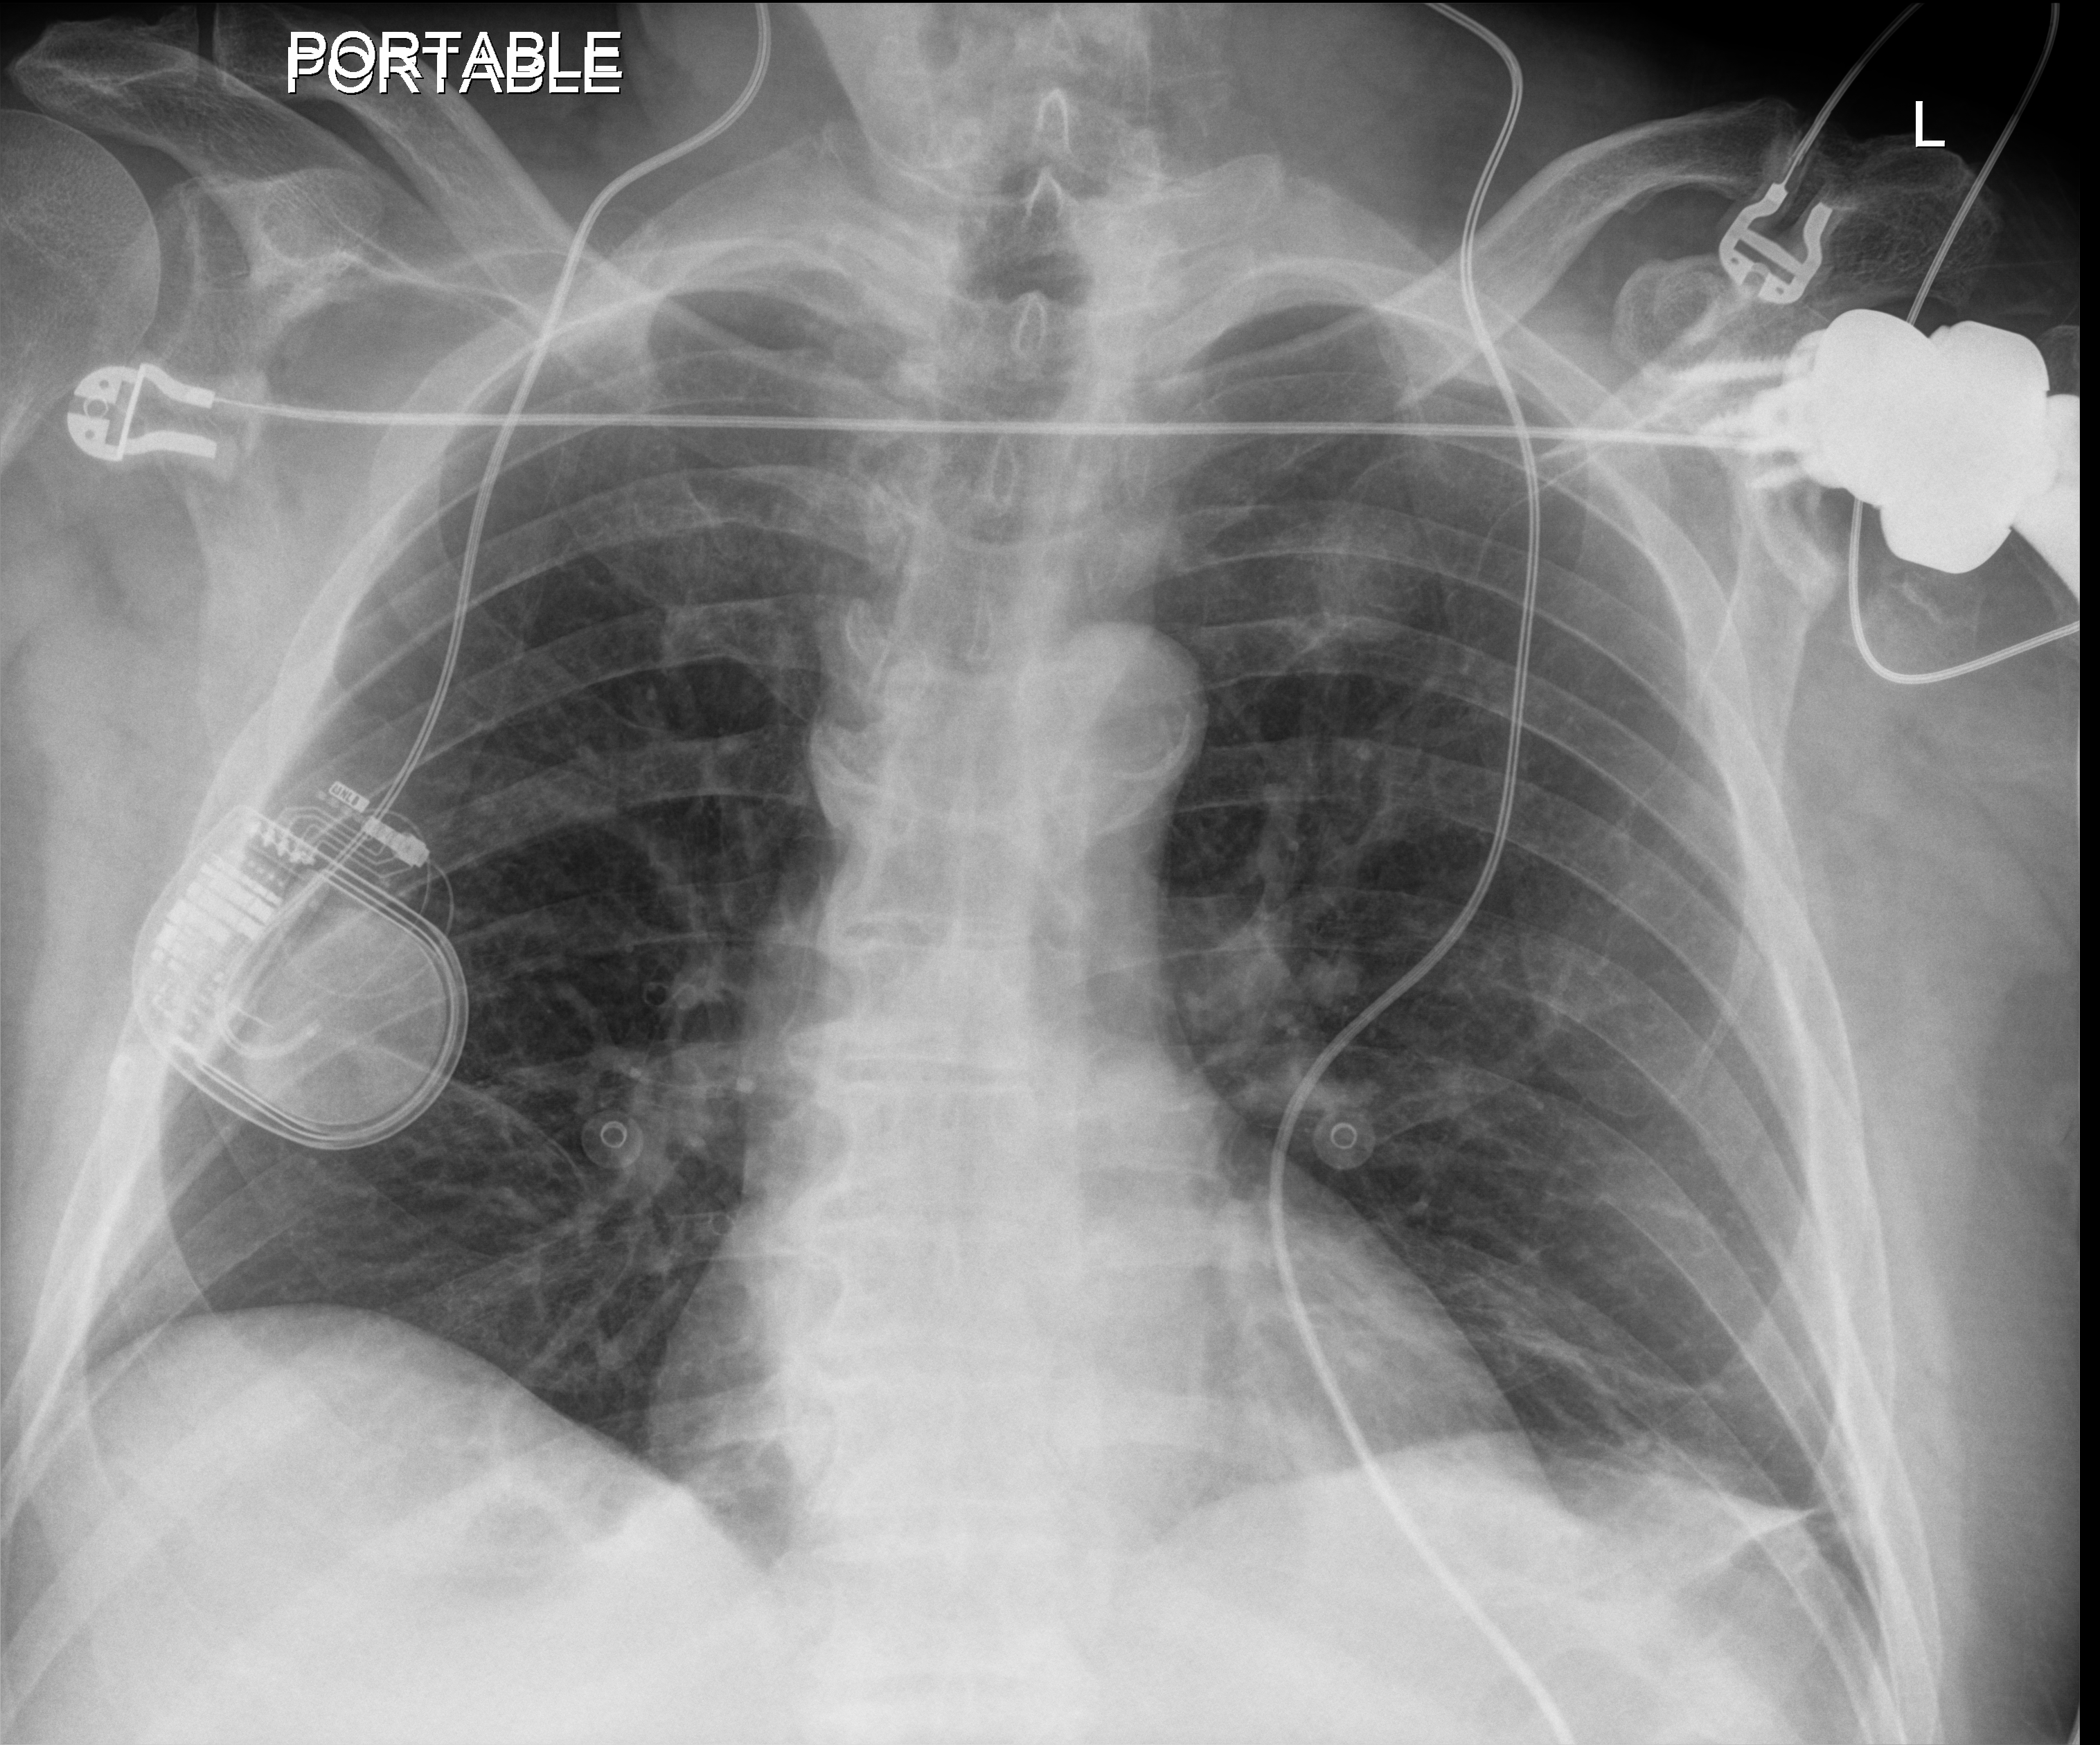
Bedside chest radiograph (digital radiography); anteroposterior (AP) projection. Patient hospitalised with COVID-19; male, aged 60–74 years.
Hospital-stay facts (about this admission, not read from this image; timing relative to this image not recorded): mechanically ventilated during this hospital stay: no; admitted to intensive care during this hospital stay: no.